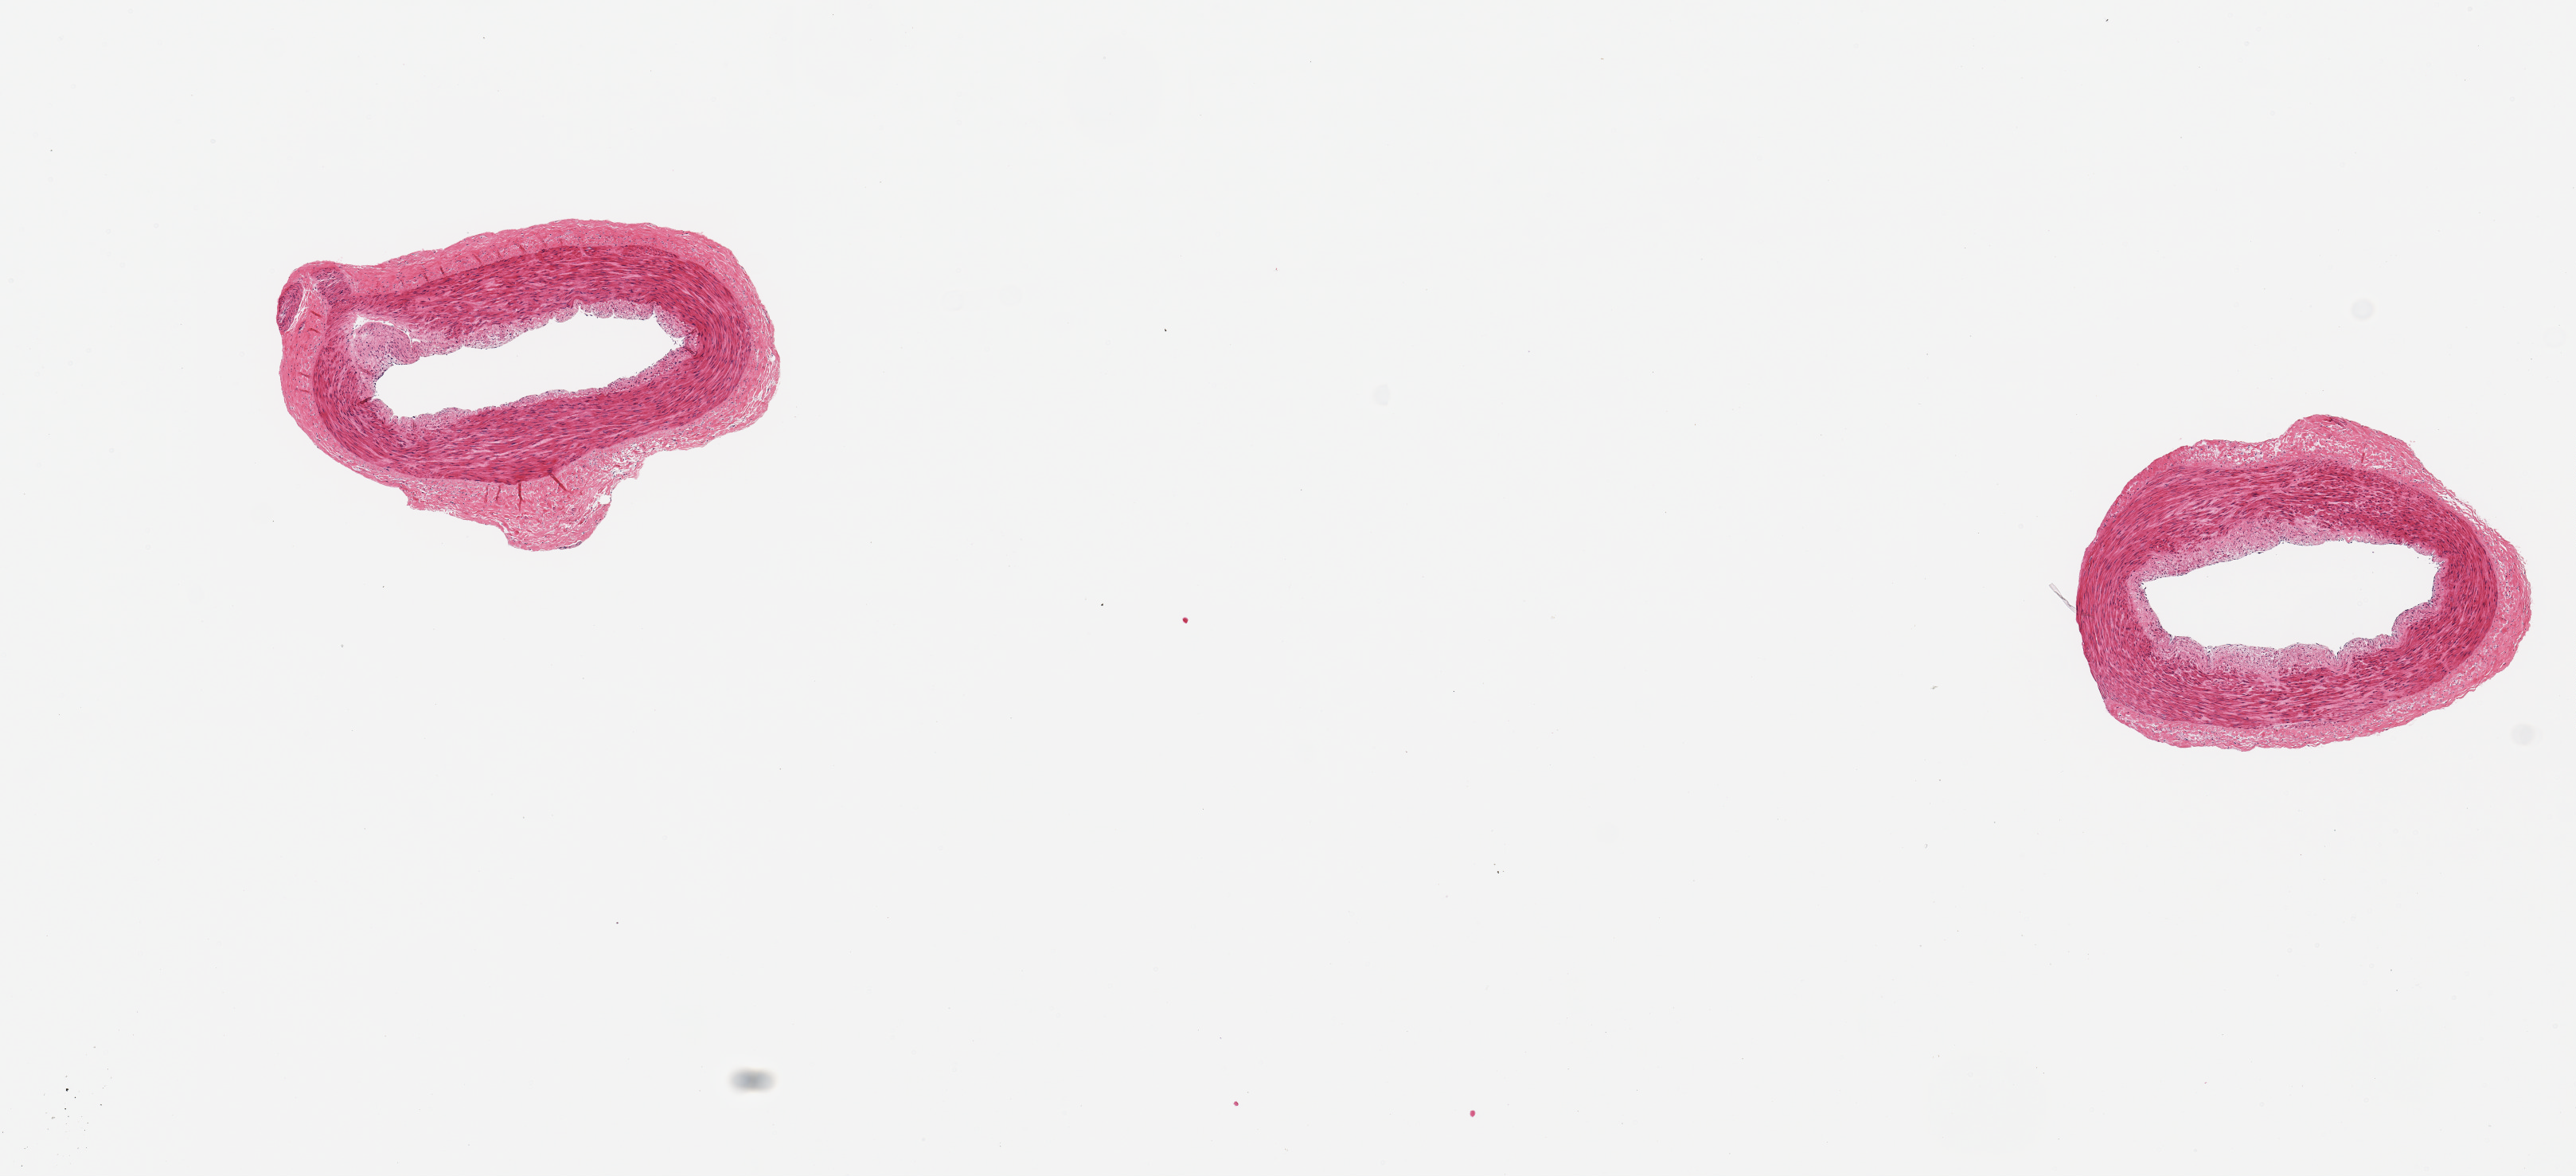
Whole-slide image, hematoxylin and eosin (H&E) stain, a low-resolution overview of the entire scanned area, about 12.8 x 5.8 mm (from a 20x scan), PAXgene-fixed, paraffin-embedded tissue, sampled site (target tissue): tibial artery, donor tissue sample. Donor sex: female.
- pathologist's review note for this sample: 2 pieces; no lesions; well dissected